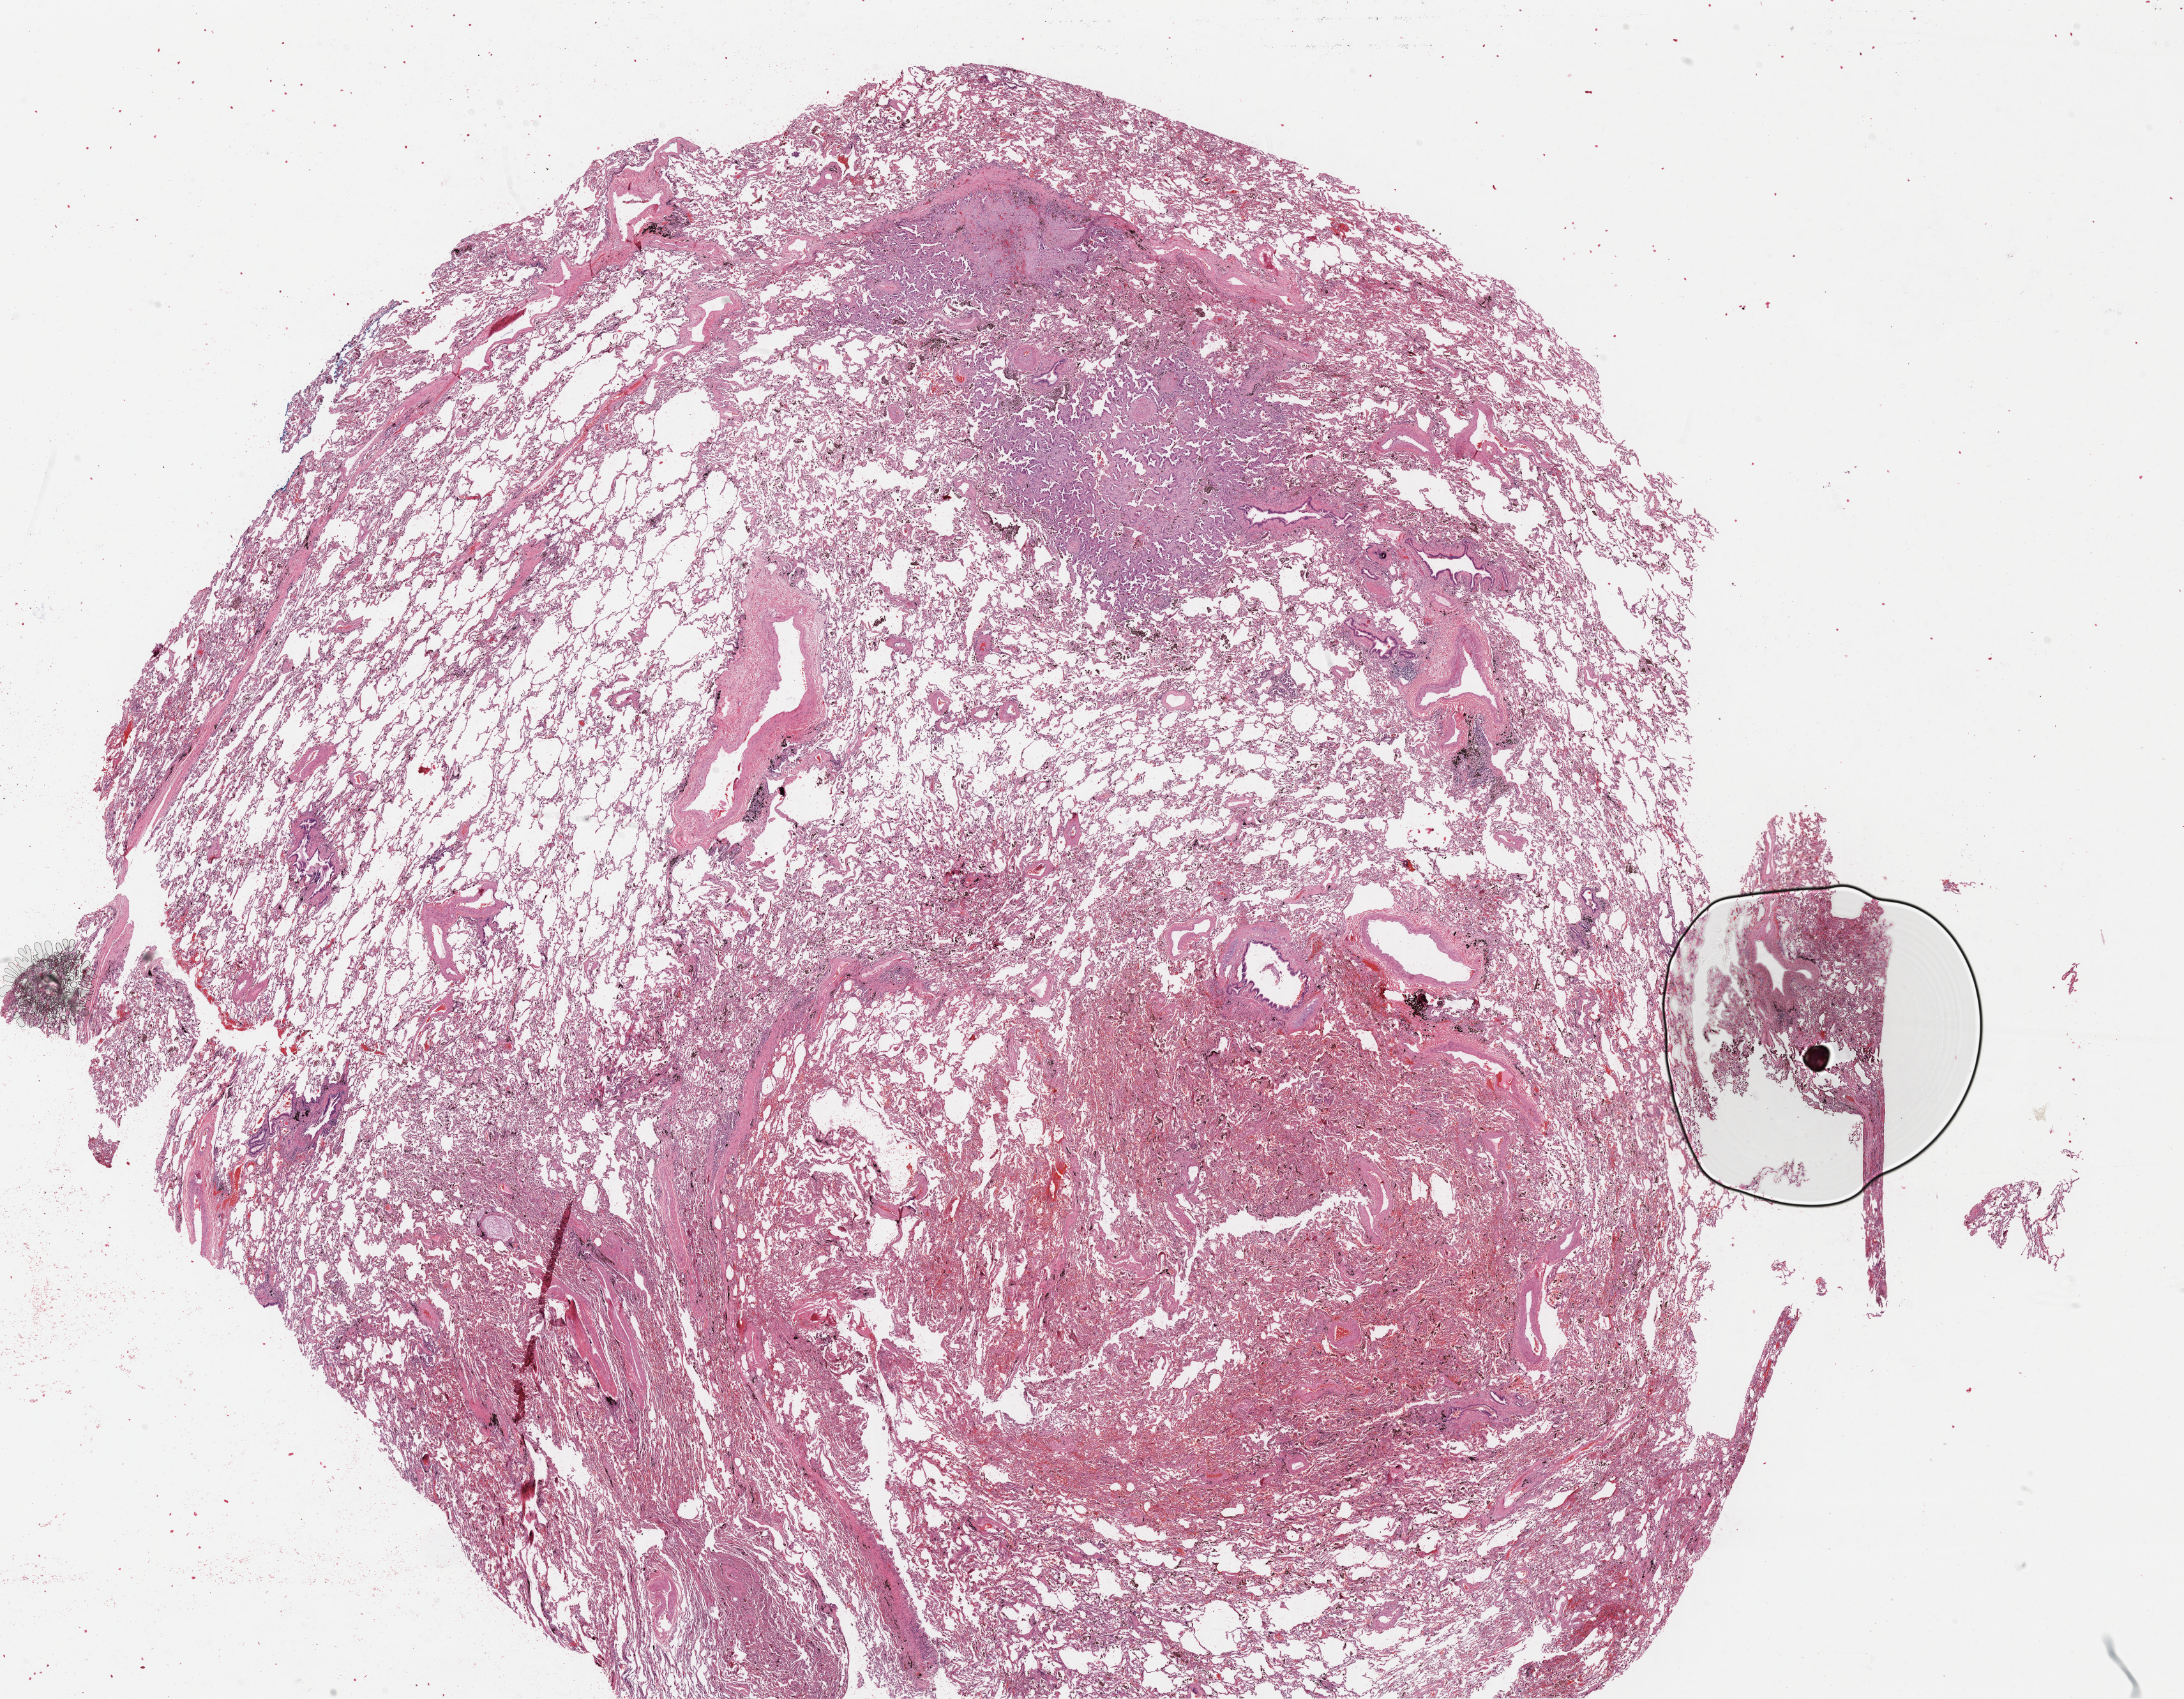
H&E whole-slide image — low-resolution overview of the scanned area, about 26.9 x 20.9 mm (from a 40x scan). FFPE section. Primary tumour sample from the lung. Female, age 61 years at initial diagnosis.
- AJCC pathologic stage: IA (7th edition)
- histologic diagnosis: Adenocarcinoma, NOS (upper lobe, lung)
- TNM: T1a N0 MX